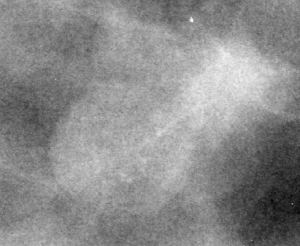
Cropped region of a digitized screen-film mammogram centred on a radiologist-marked abnormality, left breast, CC view, BI-RADS breast density category 4 (scale 1–4).
Finding: mass, shape round, margins circumscribed; BI-RADS assessment category 3; pathology result (as recorded, not read from the image): benign.